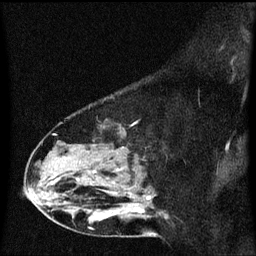
Breast MRI (dynamic contrast-enhanced), one sagittal slice; position 40 of 60 along the scan axis; dynamic contrast-enhanced series, image 2 of 3 at this slice position (ordered by acquisition); 1.5 T; TE 4.2 ms, TR 8.4 ms; 2 mm slice thickness; 256 × 256 image matrix, field of view 200 × 200 mm. Female patient, age 49 years. From the clinical record (not read from this slice): setting: breast cancer imaged before/during neoadjuvant chemotherapy; receptor status: HR-positive, HER2-negative.
Outlined on this slice (semi-automatically segmented with operator editing):
- analysis volume of interest (the breast-tissue region the enhancement analysis was run in; not a lesion): box from (x=27, y=98) to (x=169, y=221) px
- tumour enhancement mask (voxels above the 70 % enhancement threshold inside the analysis volume of interest): (x=140, y=198)–(x=152, y=213)